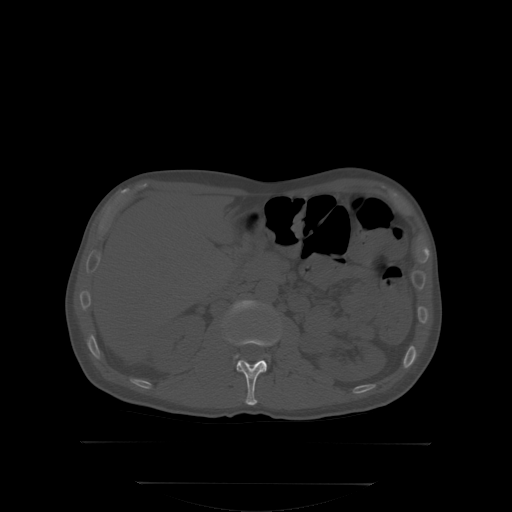
CT including the spine, one axial slice. Position 148 of 350 along the scan axis. Bone window (W 1800 / L 400 HU). 2.5 mm slice thickness. 512 × 512 image matrix. Male patient, age 58 years. Case-level facts recorded for this patient, not image findings: primary cancer: prostate; vertebrae with lytic lesions (as recorded): L1.
Annotated regions visible in this slice (semi-automatically segmented with operator editing):
- L1 vertebra: bounding box (x1, y1, x2, y2) in pixels: (226, 324, 279, 405)
- L2 vertebra: (229, 302, 266, 315)